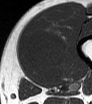
MRI of an extremity soft-tissue mass, one axial slice. Slice 17 of 62 in the series (ordered by position). MR volume resampled by the dataset authors to the PET/CT grid (not the native acquisition matrix). 3.27 mm slice thickness. 92 × 104 image matrix, field of view 90 × 102 mm. Male patient. From the clinical record (not read from this slice): histological type: mixoid liposarcoma; grade: low; site of the primary tumour: left thigh.
Outlined on this slice (expert contour drawn on MRI and transferred to this co-registered scan by the dataset authors):
- gross tumour volume (mass): box from (x=25, y=26) to (x=67, y=84) px